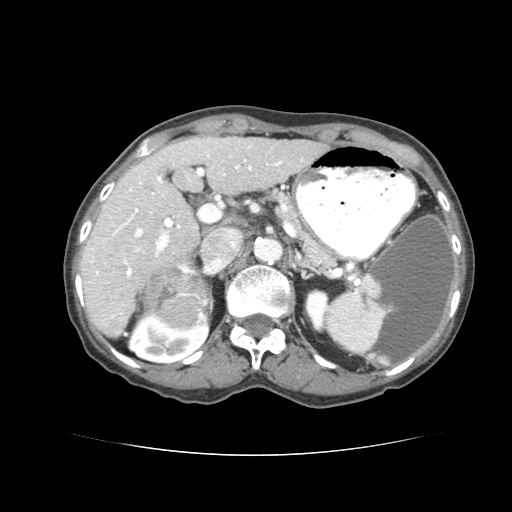
Contrast-enhanced abdominal CT (liver protocol), one axial slice. Position 44 of 77 along the scan axis. Reconstruction kernel STANDARD. Soft-tissue window (W 400 / L 40 HU). 2.5 mm slice thickness. 512 × 512 image matrix, field of view 340 × 340 mm. Case-level facts recorded for this patient, not image findings: diagnosis: hepatocellular carcinoma (patient treated with transarterial chemoembolisation; whether this scan precedes or follows treatment is not stated here); TNM stage (as recorded): Stage-I; Child-Pugh class: A; tumour nodularity: uninodular; tumour size: 7.6 cm.
Structures marked on this image (semi-automatically segmented with operator editing):
- liver parenchyma outside the tumour (the mass and vessels are separate outlines, so this box may not span the whole liver): box from (x=78, y=134) to (x=332, y=334) px
- mass: (x=144, y=269)–(x=211, y=328)
- liver vessels: (x=95, y=148)–(x=282, y=273)